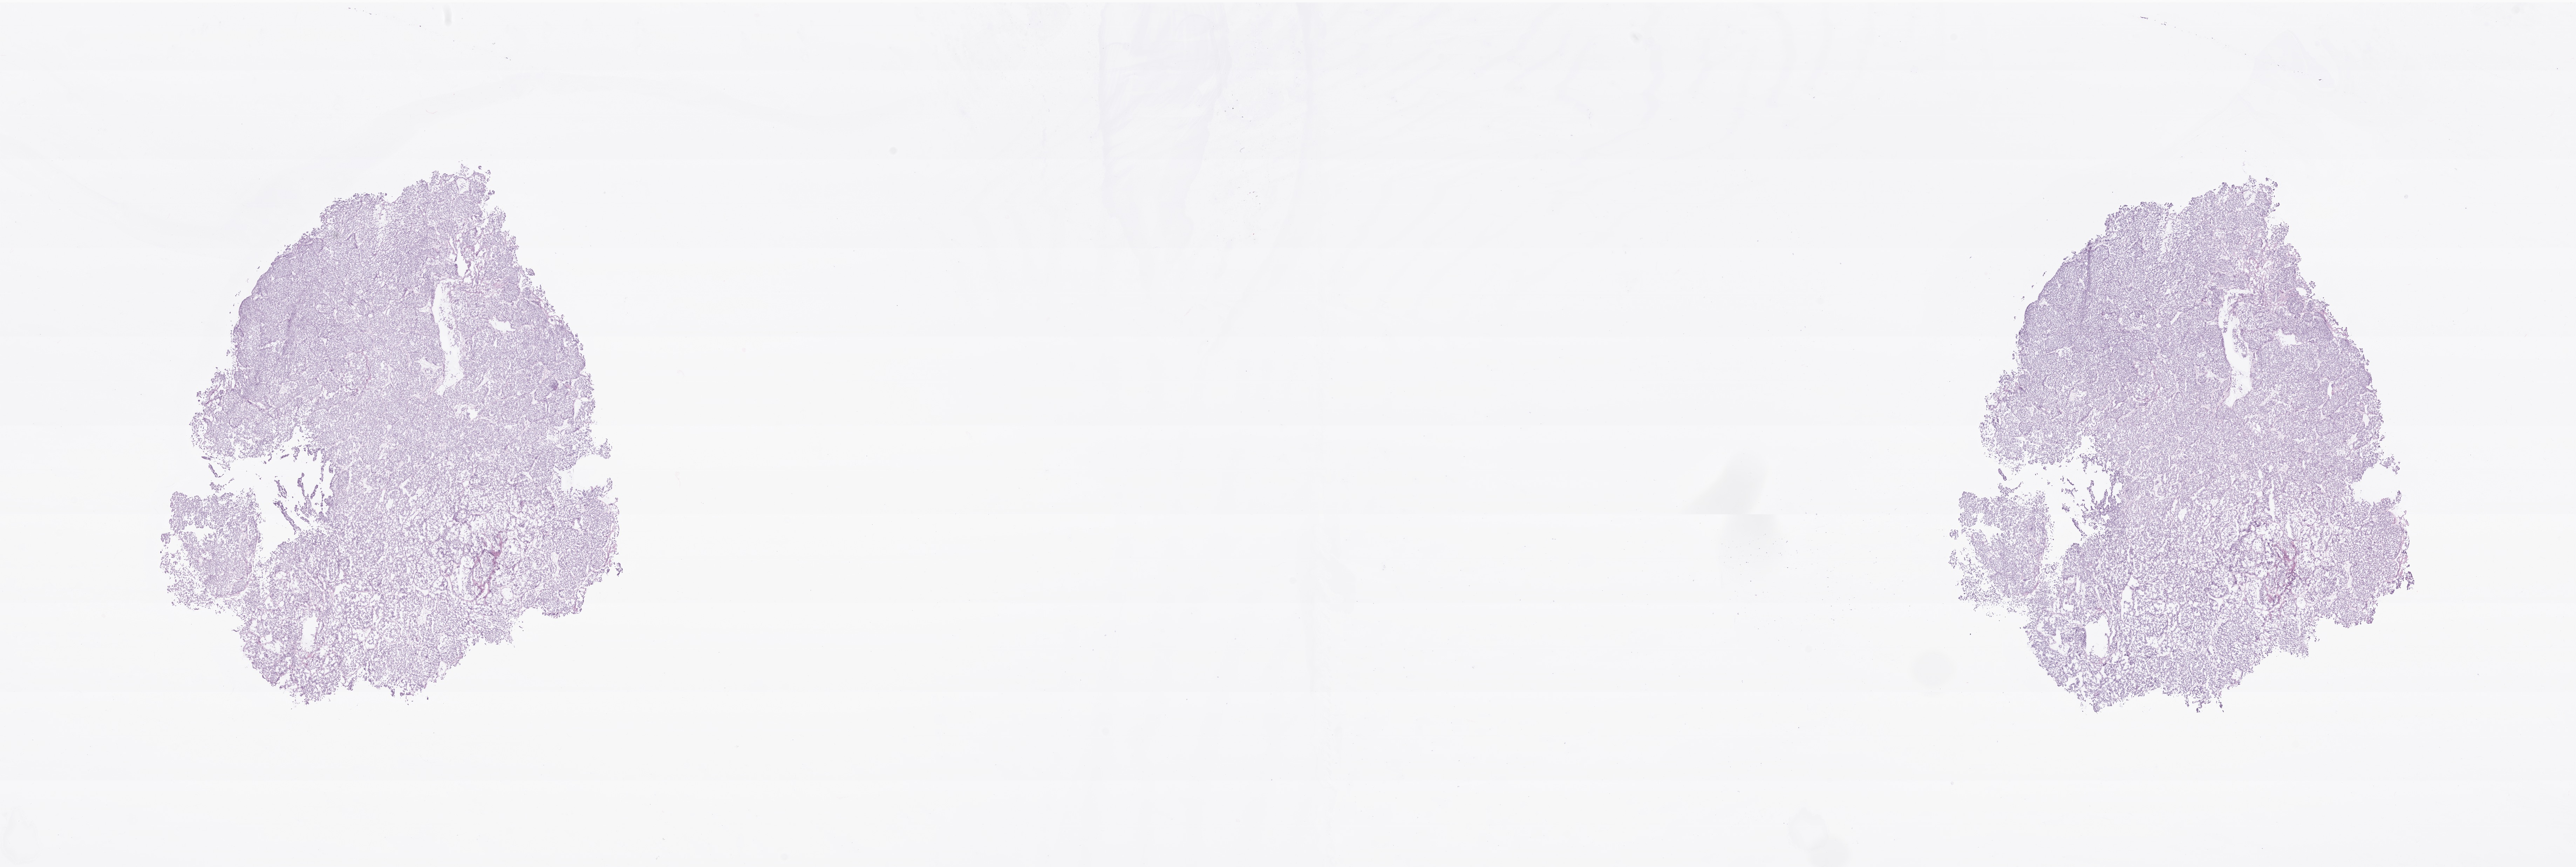
Digitized H&E-stained section of tumor tissue from the tail of pancreas — low-resolution overview of the scanned area, about 30.9 x 10.4 mm; cryosection (OCT / tissue freezing medium). Patient: female, age 139 months (11 years 7 months).
Recorded diagnosis: Acinar cell carcinoma.